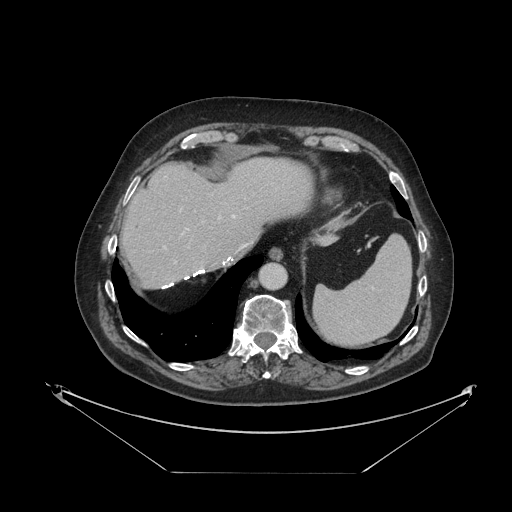
Contrast-enhanced abdominal CT, one axial slice. Position 95 of 121 along the scan axis. Reconstruction kernel STANDARD. 120 kVp. Intravenous contrast given. Soft-tissue window (W 400 / L 40 HU). 512 × 512 image matrix. Male patient, age 68 years. Case-level facts recorded for this patient, not image findings: diagnosis: colorectal cancer liver metastases, imaged before liver resection; multiple liver metastases: no; largest metastasis: 4 cm.
Structures marked on this image (expert manual segmentation):
- hepatic veins: bounding box (x1, y1, x2, y2) in pixels: (183, 215, 246, 246)
- liver: (123, 158, 314, 288)
- planned liver remnant (the part of the liver to remain after resection): (122, 157, 314, 288)
- portal vein (with intrahepatic branches): (164, 216, 221, 264)